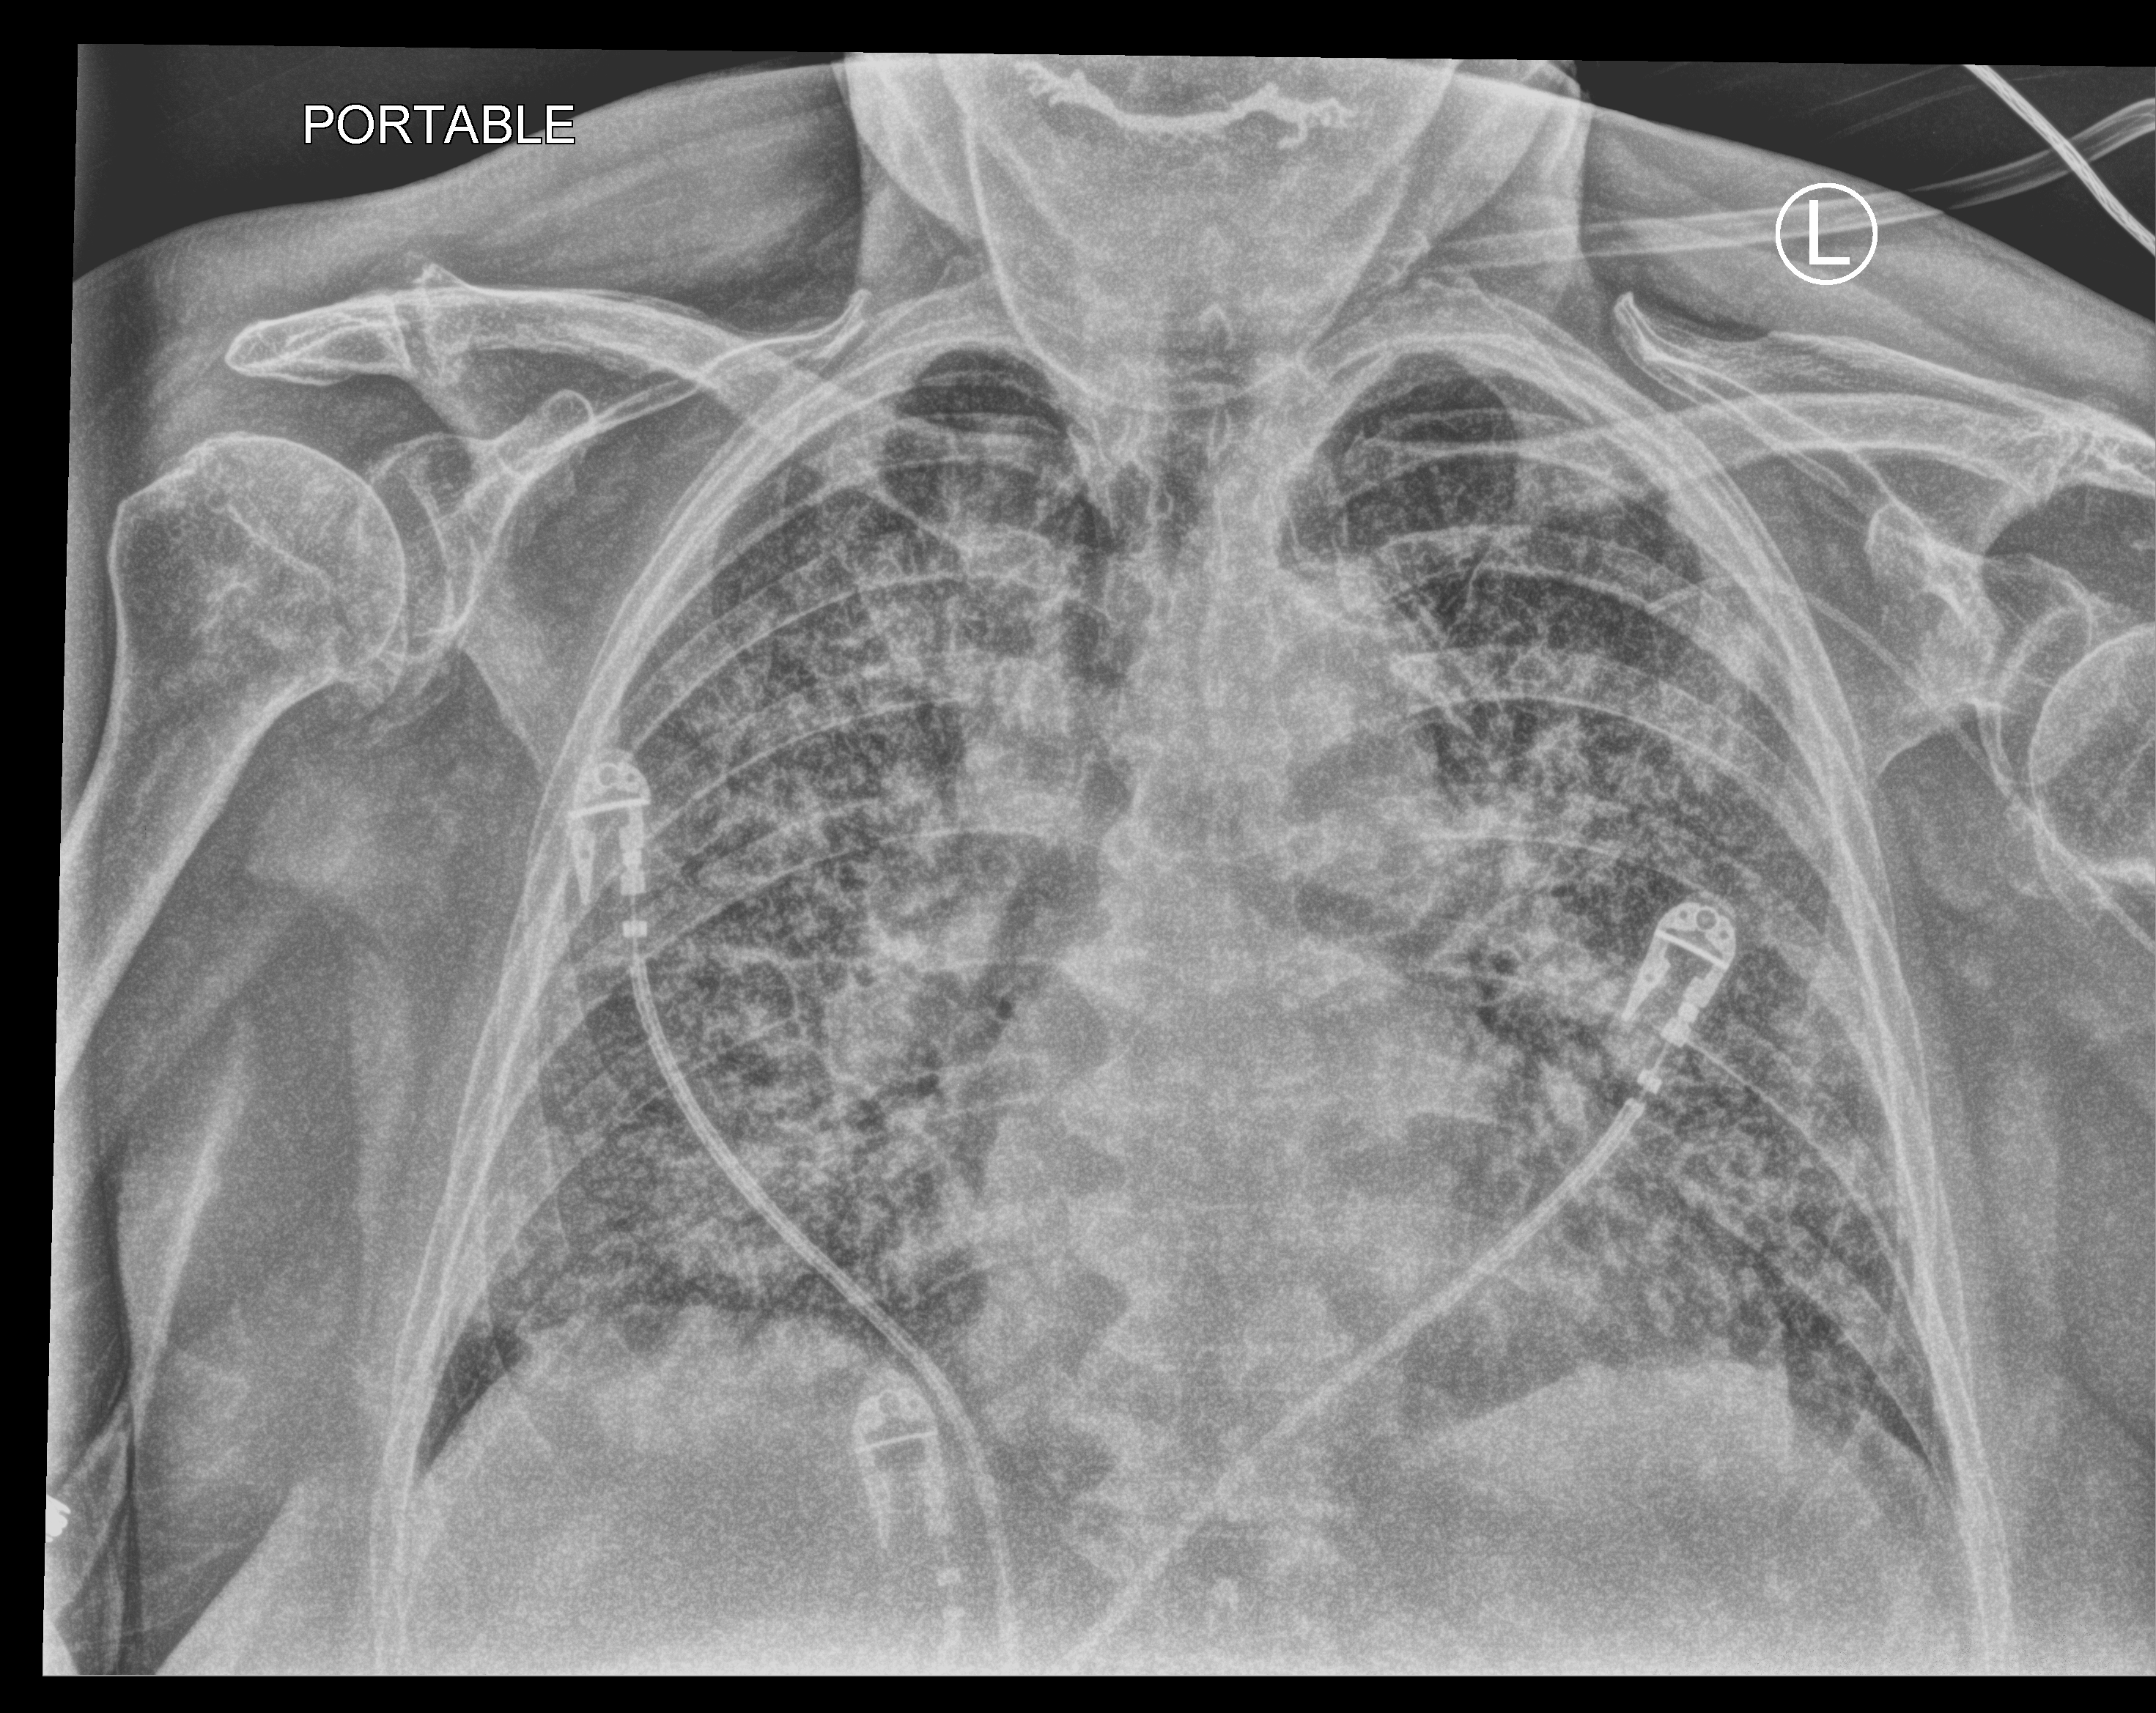
Portable chest radiograph; anteroposterior (AP) projection. Patient hospitalised with COVID-19; female, aged 75–90 years.
From the hospital-stay record, not from the radiograph (when in the stay this image was taken is not recorded):
- mechanically ventilated during this hospital stay: yes
- length of hospital stay: 56 days
- admitted to intensive care during this hospital stay: no